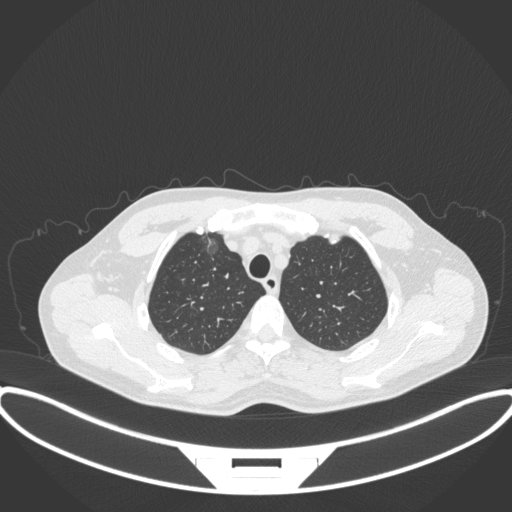
Chest CT, one axial slice; slice 304 of 395 in the series (ordered by position); 120 kVp; lung window (W 1500 / L -600 HU); 1 mm slice thickness; 512 × 512 image matrix. Patient: male, 60 years. From the clinical record (not read from this slice): clinical TNM (as recorded): T1c N0 M0.
Structures marked on this image (bounding box drawn by a radiologist):
- lung tumour (recorded histology: adenocarcinoma): bounding box <202,233,222,260> (left, top, right, bottom; pixels)